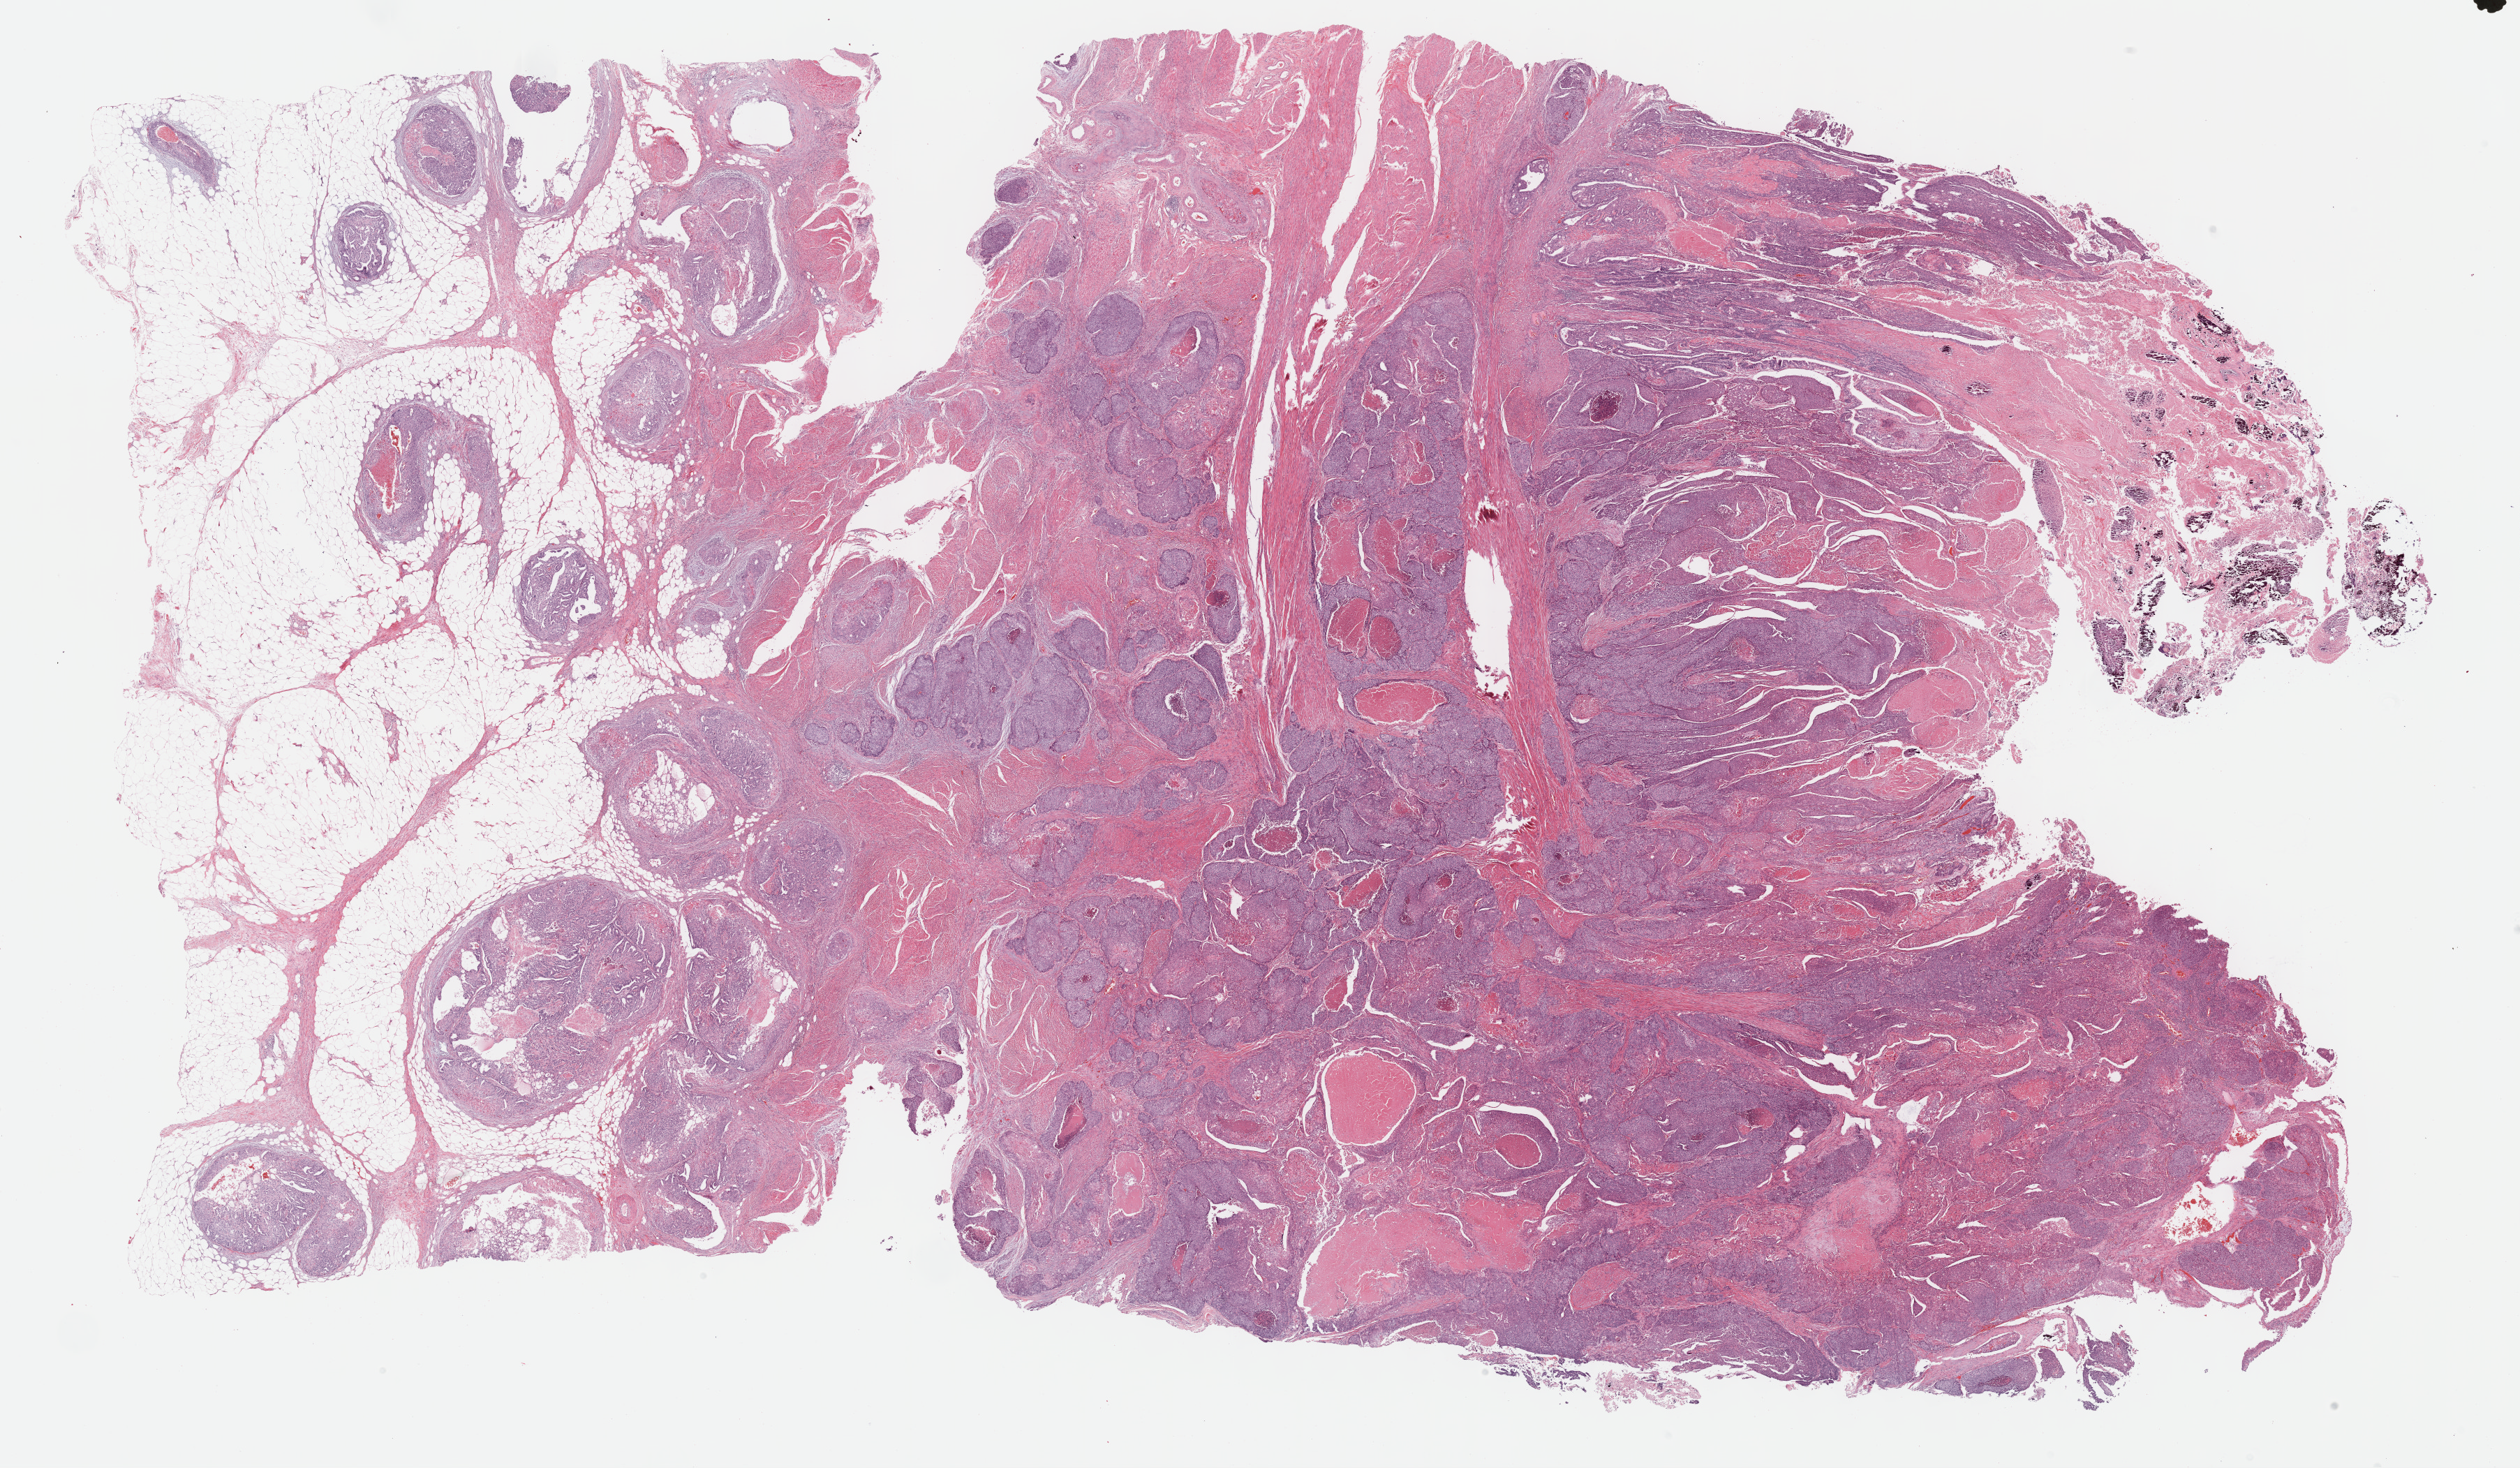
Digitized Hematoxylin and eosin (H&E) stained tissue section (whole slide) — low-resolution overview of the scanned area, about 29.2 x 17.0 mm. FFPE section. Bladder, primary tumour sample. Male, age 80 years at initial diagnosis. Histologic grade: high grade.
Lymph nodes positive (case pathology): 4 of 43 examined. AJCC pathologic stage: IV (6th edition). Pathologic diagnosis: Transitional cell carcinoma.